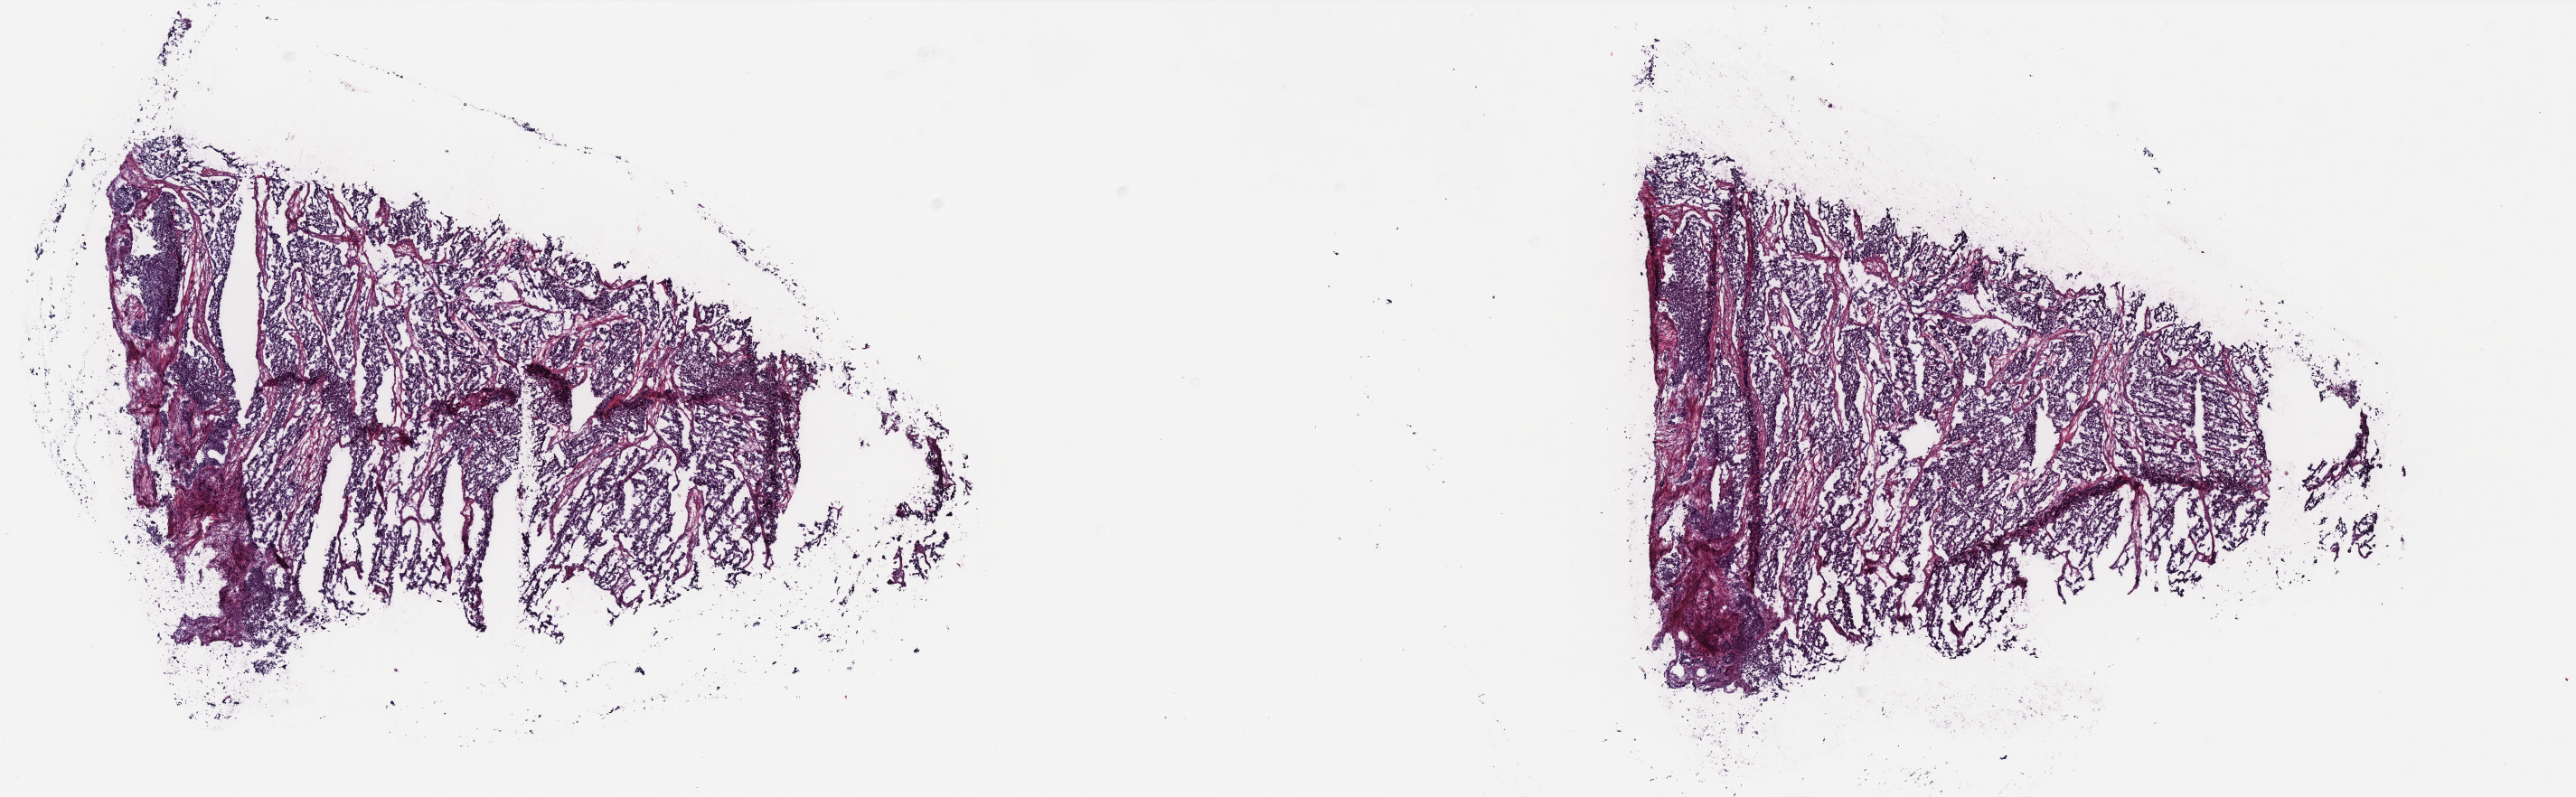
Digitized Hematoxylin and eosin (H&E) stained tissue section (whole slide) — low-resolution overview of the scanned area, about 22.8 x 7.1 mm; frozen section from the top of the tissue portion; sample: primary tumour, uterus. Female, age 63 years at initial diagnosis.
Pathologic diagnosis: Endometrioid adenocarcinoma, NOS (endometrium).